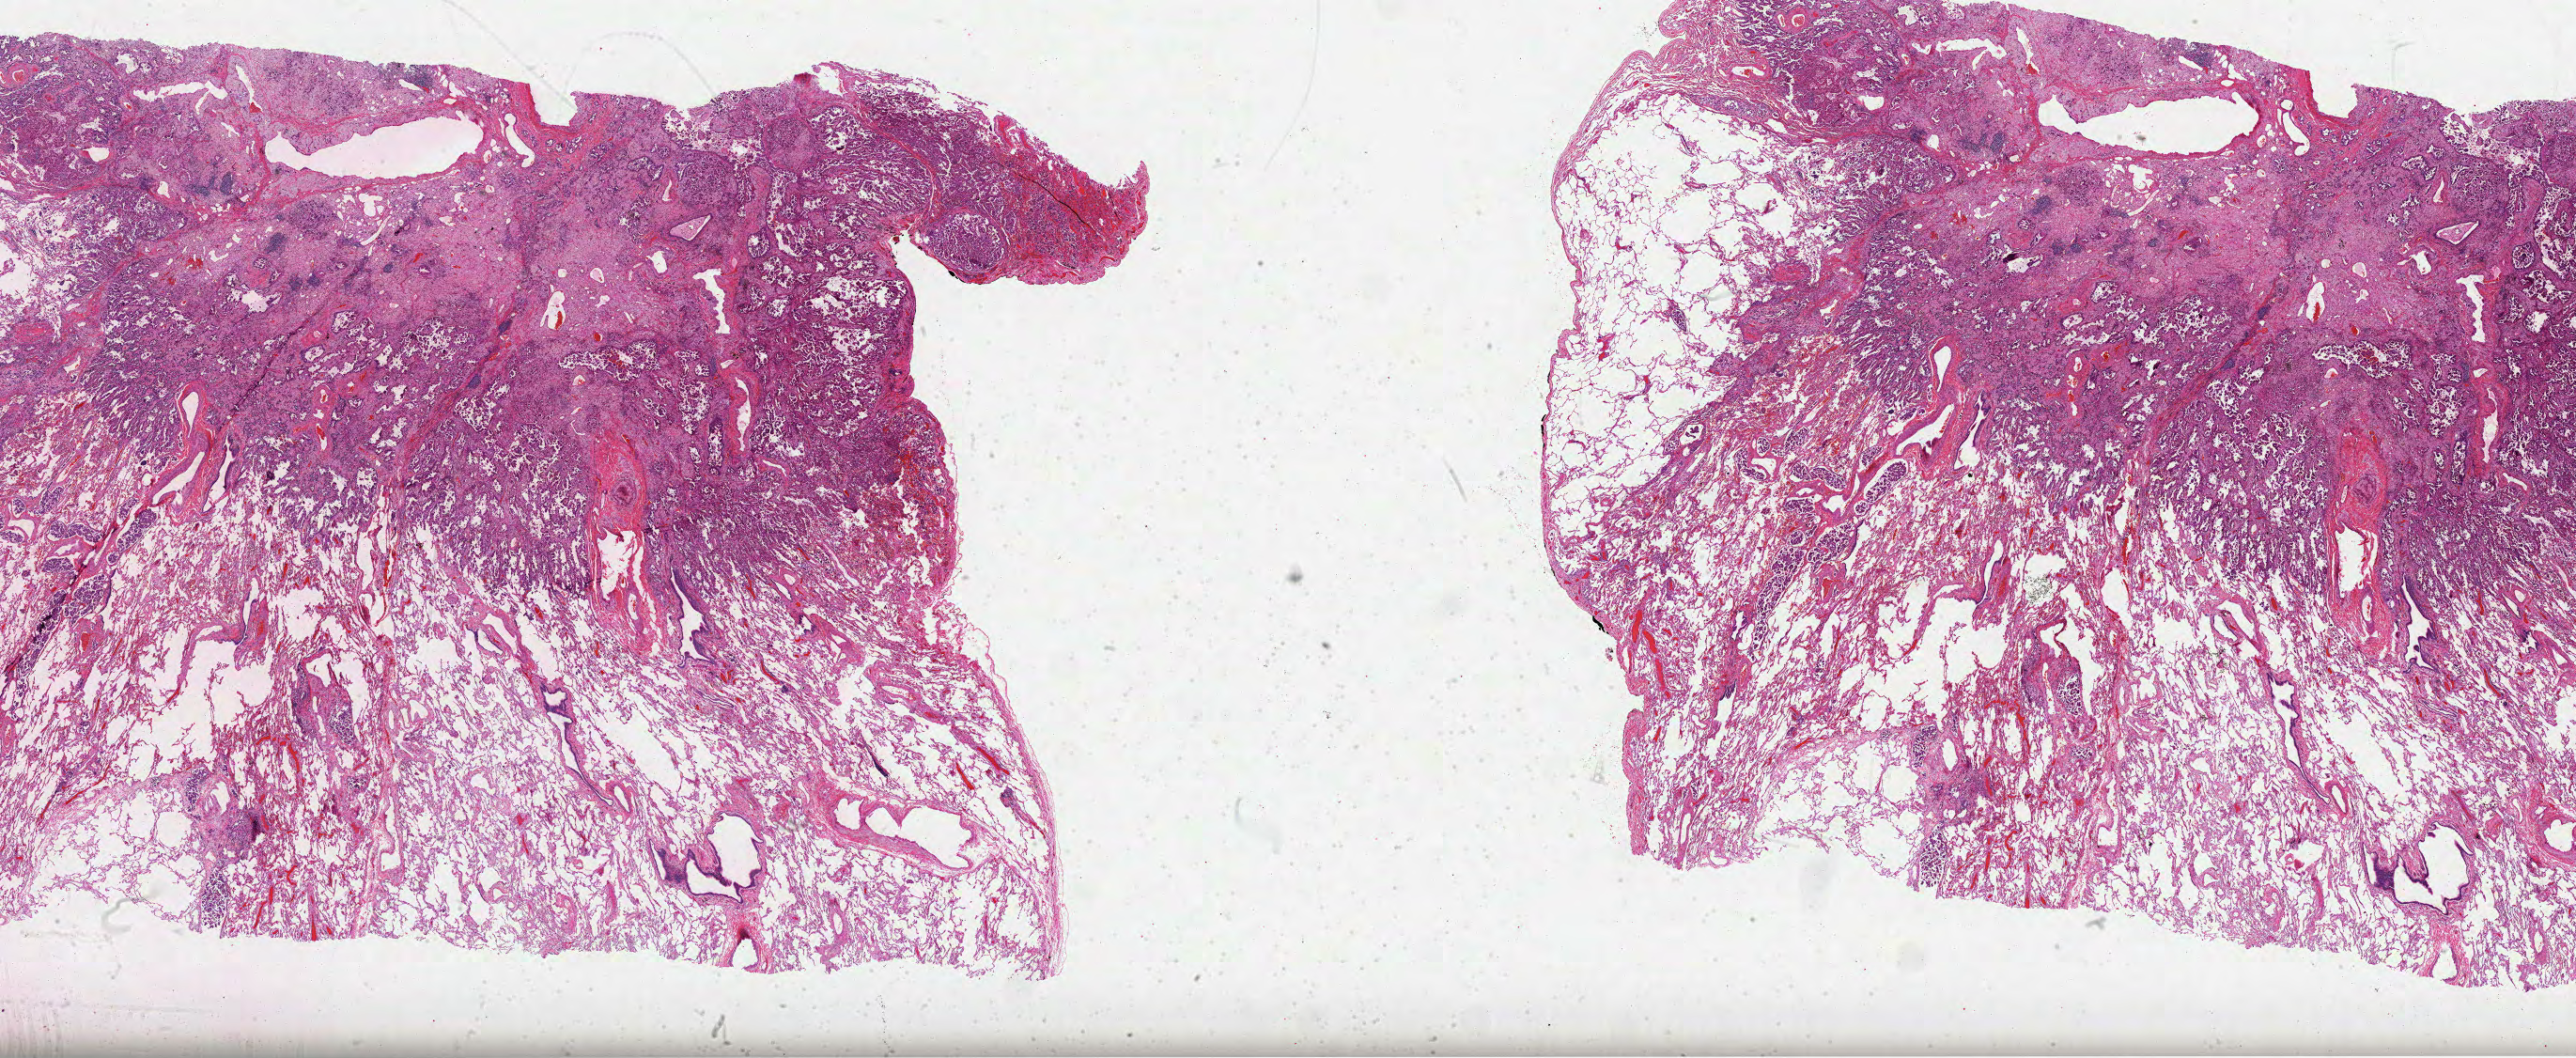
Hematoxylin and eosin (H&E) stained whole-slide image — a low-resolution overview of the entire scanned area, about 44.2 x 18.2 mm (acquisition: 40x scan). Formalin-fixed paraffin-embedded (FFPE) diagnostic section. Lung, primary tumour sample. Patient: female, age at initial diagnosis 69 years.
TNM: T2 N2 MX. Laterality: right. AJCC pathologic stage: IIIA (6th edition). Pathologic diagnosis: Adenocarcinoma, NOS (middle lobe, lung).